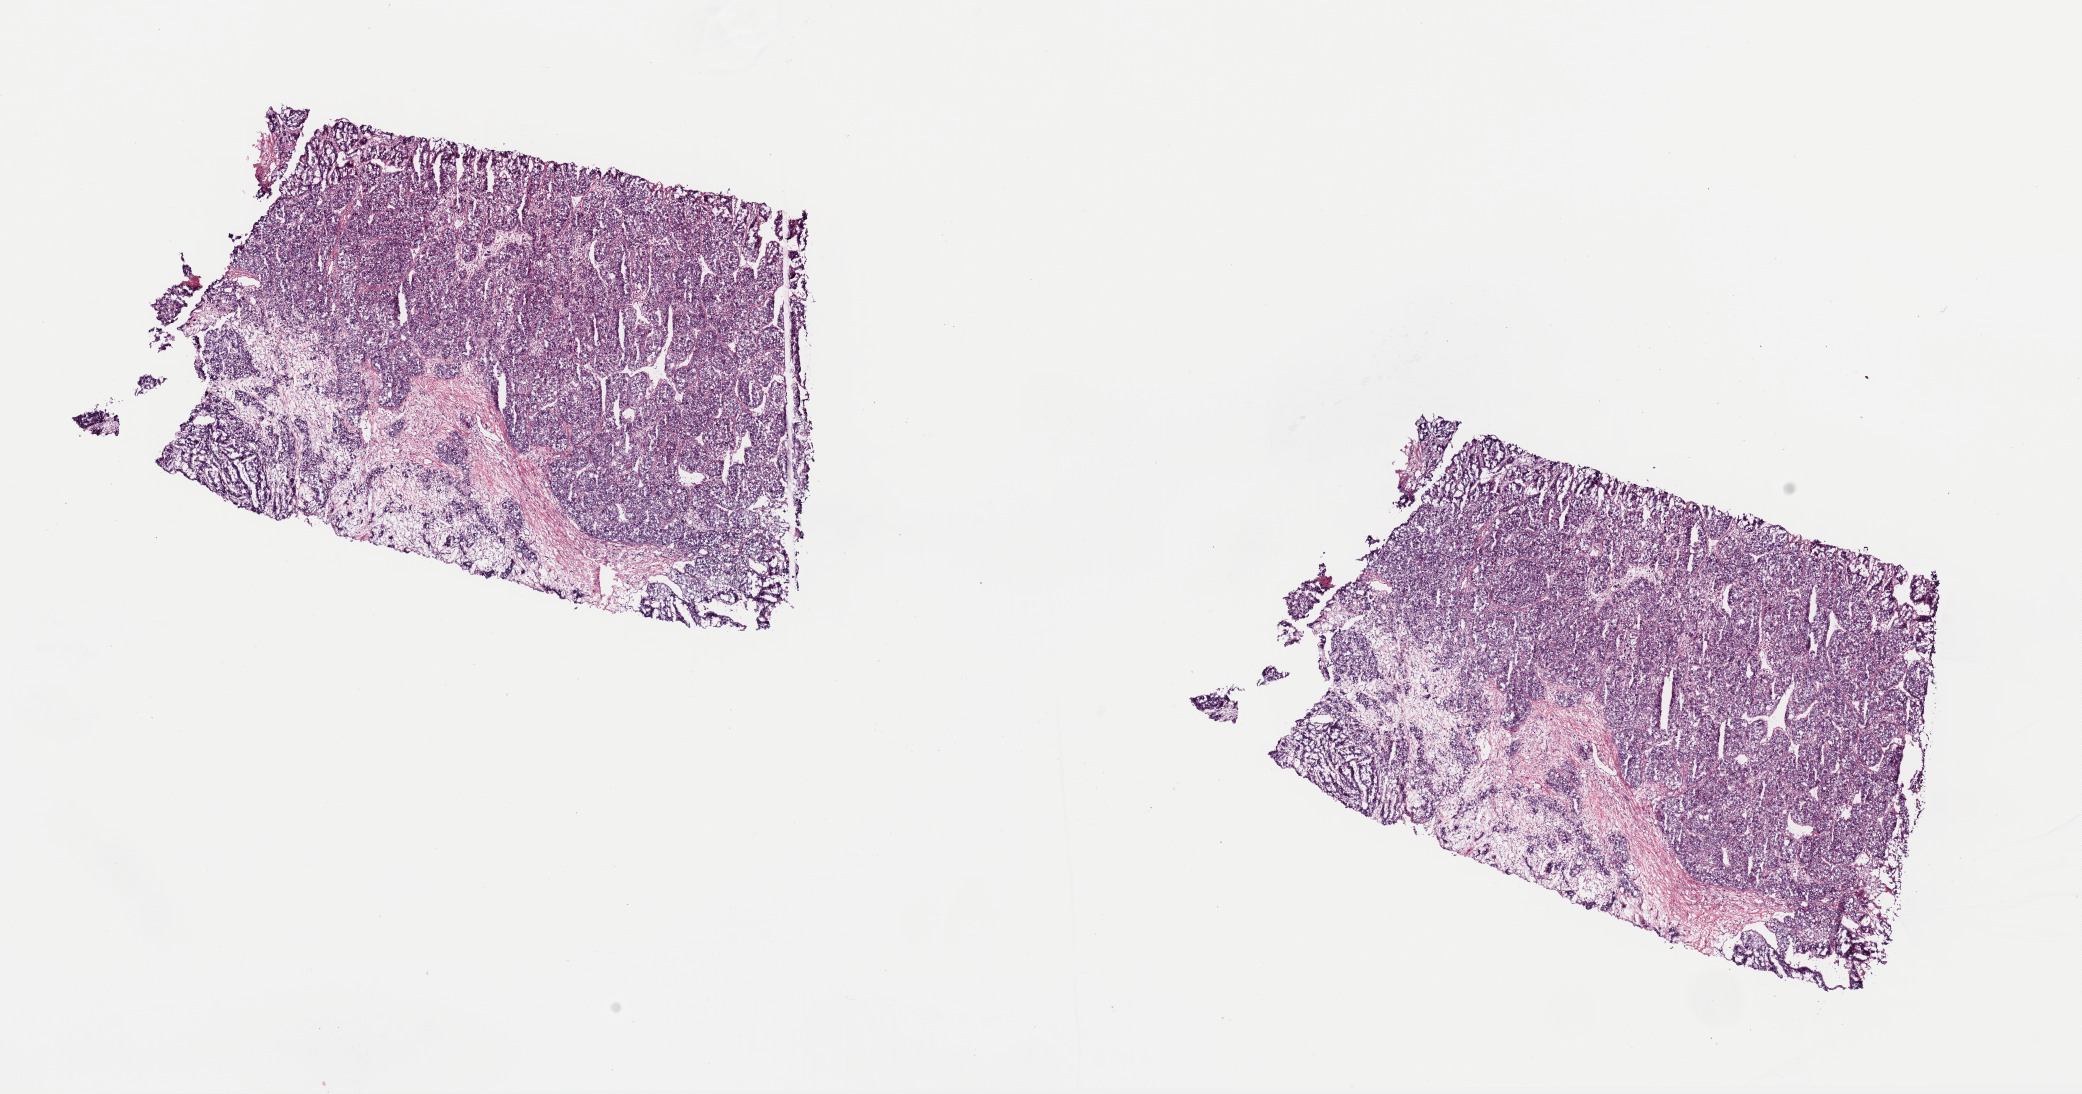
Whole-slide histology image, H&E — whole scanned area (about 16.4 x 8.6 mm, acquisition: 40x scan) shown as a low-resolution overview, frozen section, liver, primary tumour sample. Female, age 65 years at initial diagnosis. Composition of this section per pathologist review: tumour cells 75%, tumour nuclei 100%.
Pathologic diagnosis: Hepatocellular carcinoma, NOS.